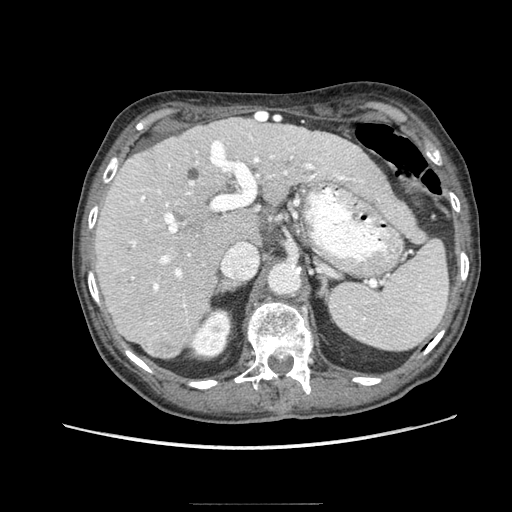
Contrast-enhanced abdominal CT (liver protocol), one axial slice; slice 54 of 83 in the series (ordered by position); 140 kVp; soft-tissue window (W 400 / L 40 HU); 2.5 mm slice thickness; 512 × 512 image matrix, field of view 360 × 360 mm. From the clinical record (not read from this slice): diagnosis: hepatocellular carcinoma (patient treated with transarterial chemoembolisation; whether this scan precedes or follows treatment is not stated here); TNM stage (as recorded): Stage-I.
Annotated regions visible in this slice (semi-automatic segmentation, software-assisted and operator-edited):
- liver parenchyma outside the tumour (the mass and vessels are separate outlines, so this box may not span the whole liver): box from (x=94, y=118) to (x=389, y=358) px
- mass: (x=147, y=334)–(x=179, y=357)
- liver vessels: (x=122, y=134)–(x=338, y=325)